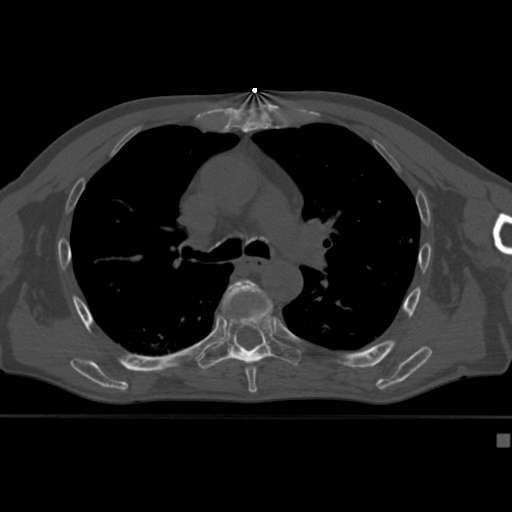
CT including the spine, one axial slice. Reconstruction kernel Br40s. 120 kVp. Bone window (W 1800 / L 400 HU). 1.5 mm slice thickness. 512 × 512 image matrix, field of view 337 × 337 mm. Patient: male, 64 years. From the clinical record (not read from this slice): primary cancer: uterus; vertebrae with lytic lesions (as recorded): T1, T4, T5, T7, L5.
Structures marked on this image (semi-automatic segmentation, software-assisted and operator-edited):
- T6 vertebra: box from (x=222, y=280) to (x=273, y=382) px
- T7 vertebra: (x=196, y=306)–(x=301, y=373)